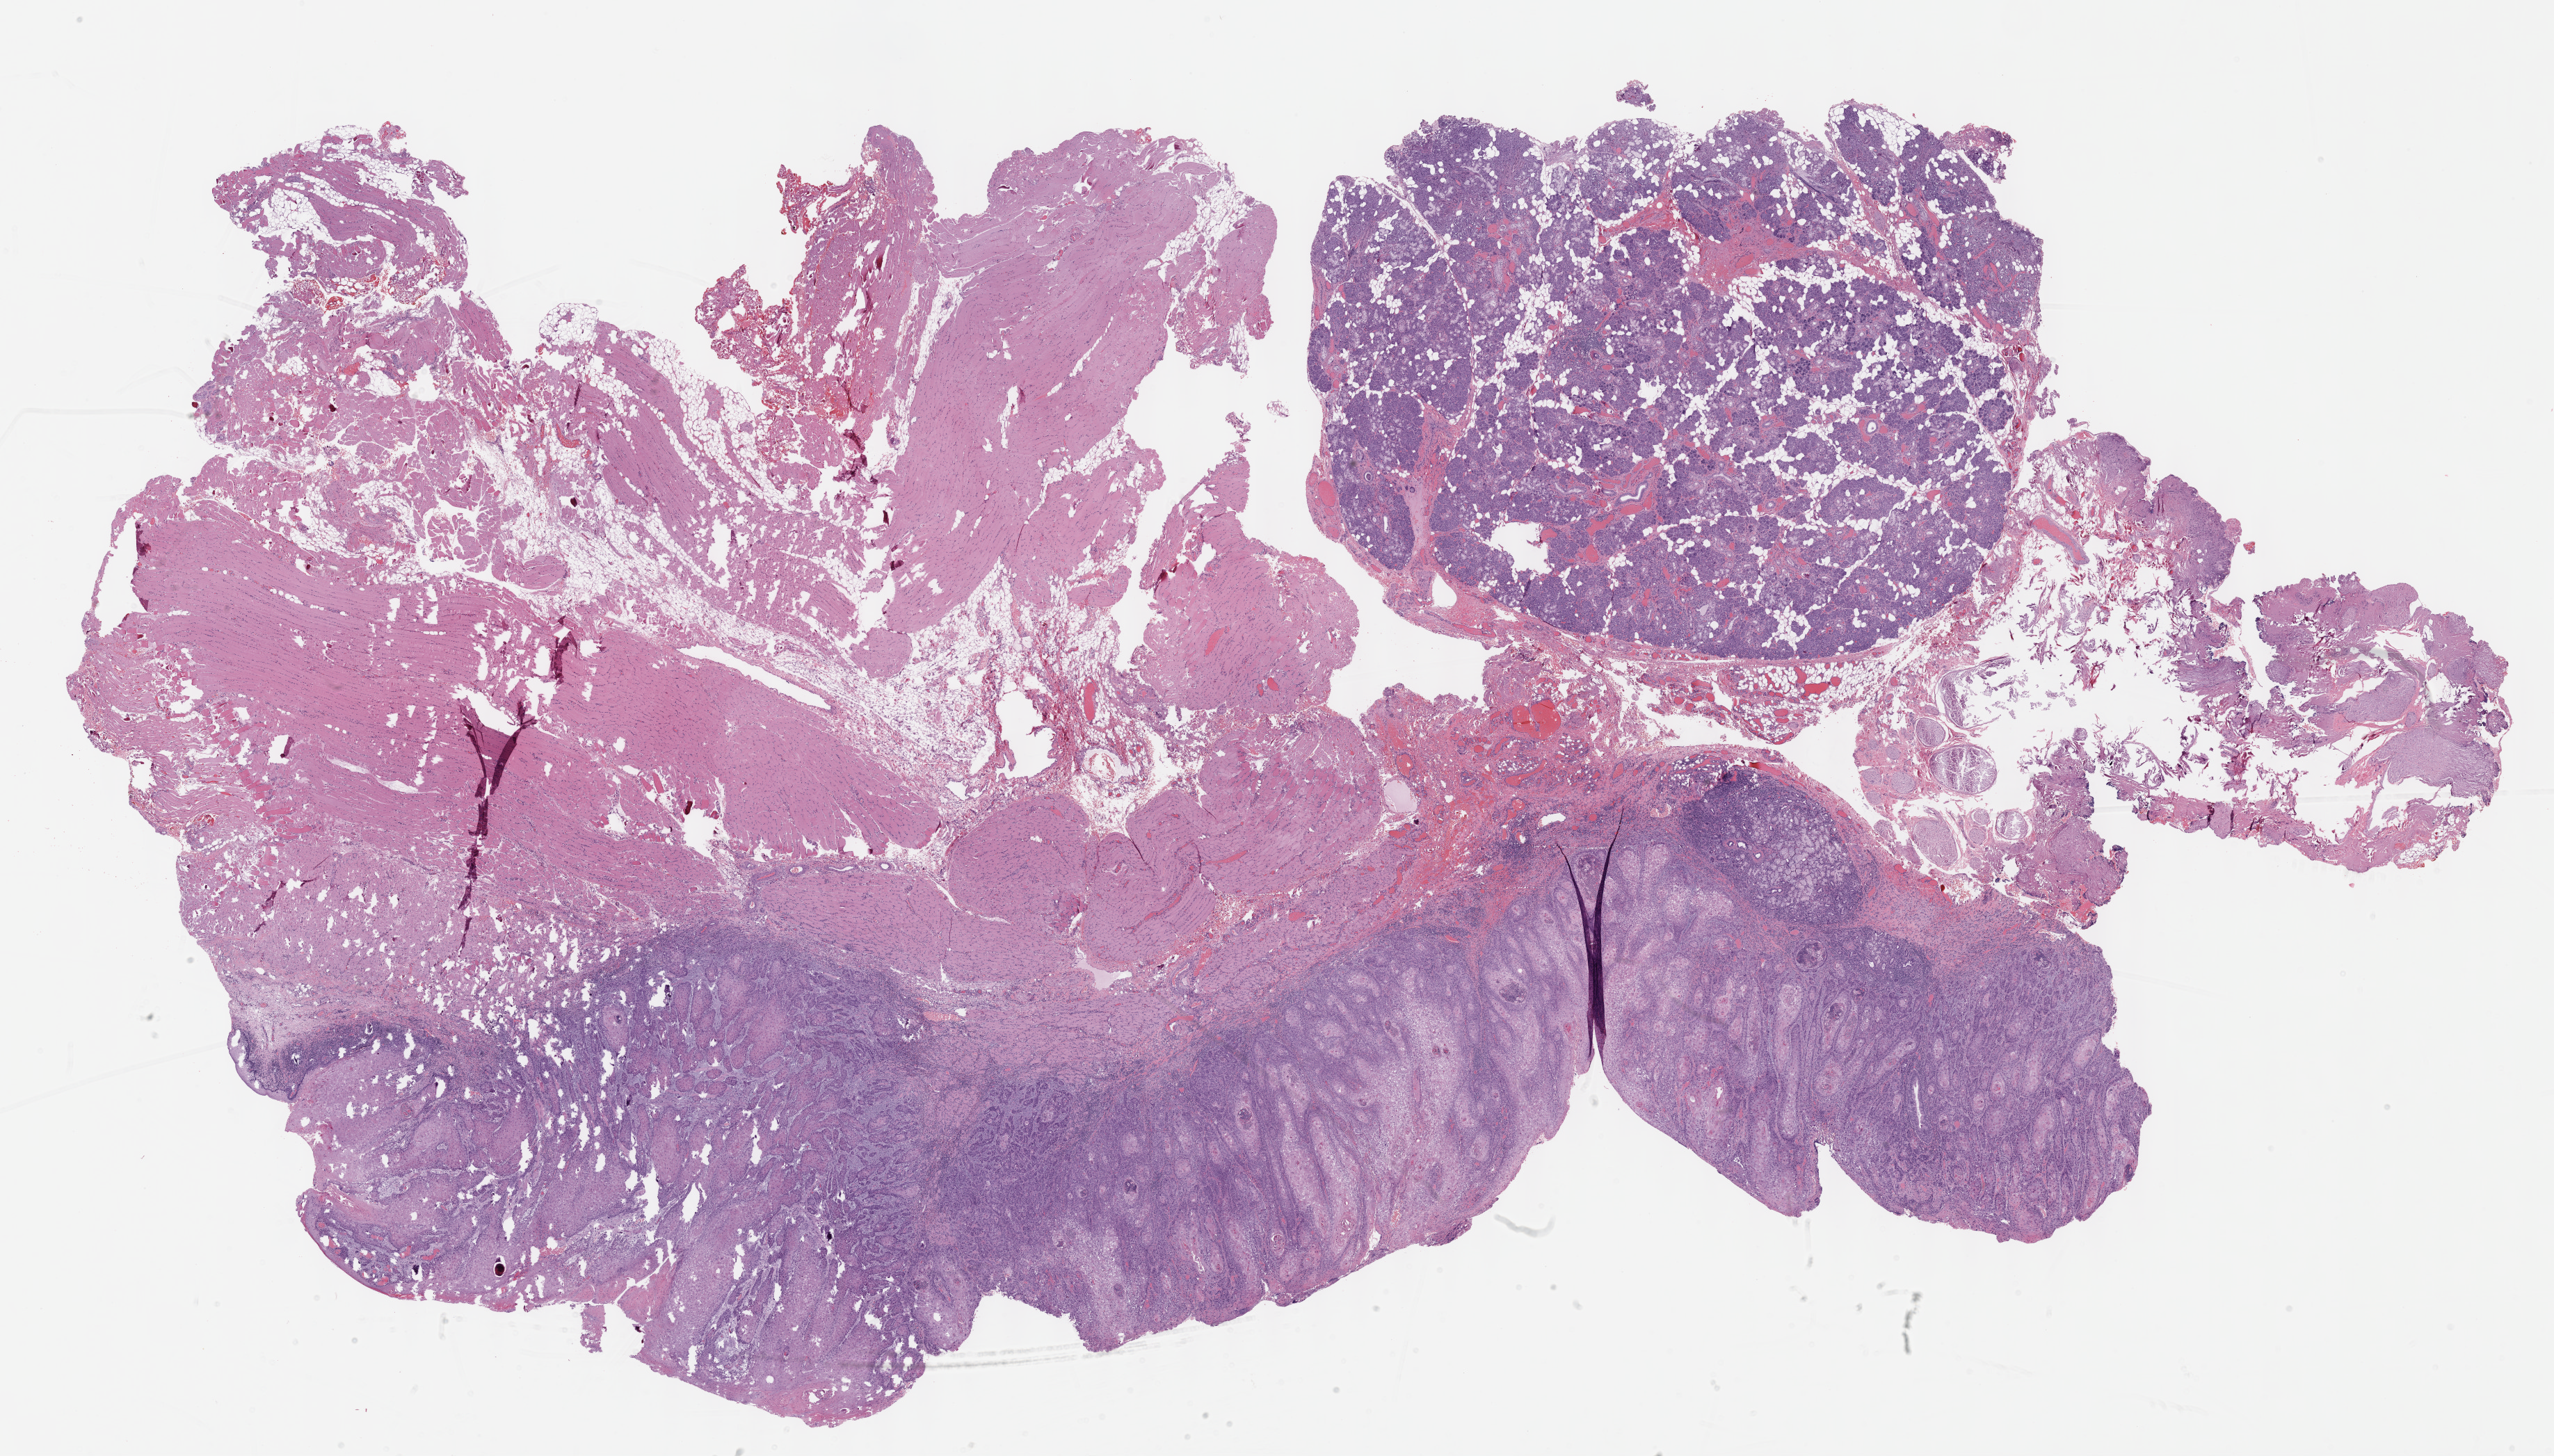
Digitized H&E-stained tissue section (whole slide), shown as a low-resolution overview of the whole scanned area (about 29.7 x 16.9 mm, from a 40x scan); formalin-fixed paraffin-embedded (FFPE) diagnostic section; primary tumour sample from the head and neck. Patient: male, age at initial diagnosis 53 years. Histologic grade: G1 (well differentiated).
Histologic diagnosis: Squamous cell carcinoma, NOS (mouth, NOS).